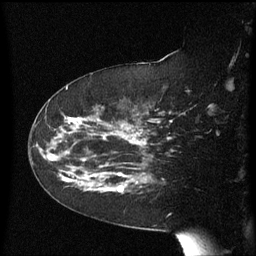
Breast MRI (dynamic contrast-enhanced), one sagittal slice; slice 38 of 60 in the series (ordered by position); dynamic contrast-enhanced series, image 2 of 3 at this slice position (ordered by acquisition); 1.5 T; TE 4.2 ms, TR 8.4 ms; 2.3 mm slice thickness; 256 × 256 image matrix, field of view 200 × 200 mm. Female patient, age 63 years. Case-level facts recorded for this patient, not image findings: setting: breast cancer imaged before/during neoadjuvant chemotherapy; receptor status: HER2-positive.
Annotated regions visible in this slice (semi-automatic segmentation, software-assisted and operator-edited):
- analysis volume of interest (the breast-tissue region the enhancement analysis was run in; not a lesion): bounding box [x1, y1, x2, y2] px = [63, 144, 147, 206]
- tumour enhancement mask (voxels above the 70 % enhancement threshold inside the analysis volume of interest): [63, 145, 142, 193]